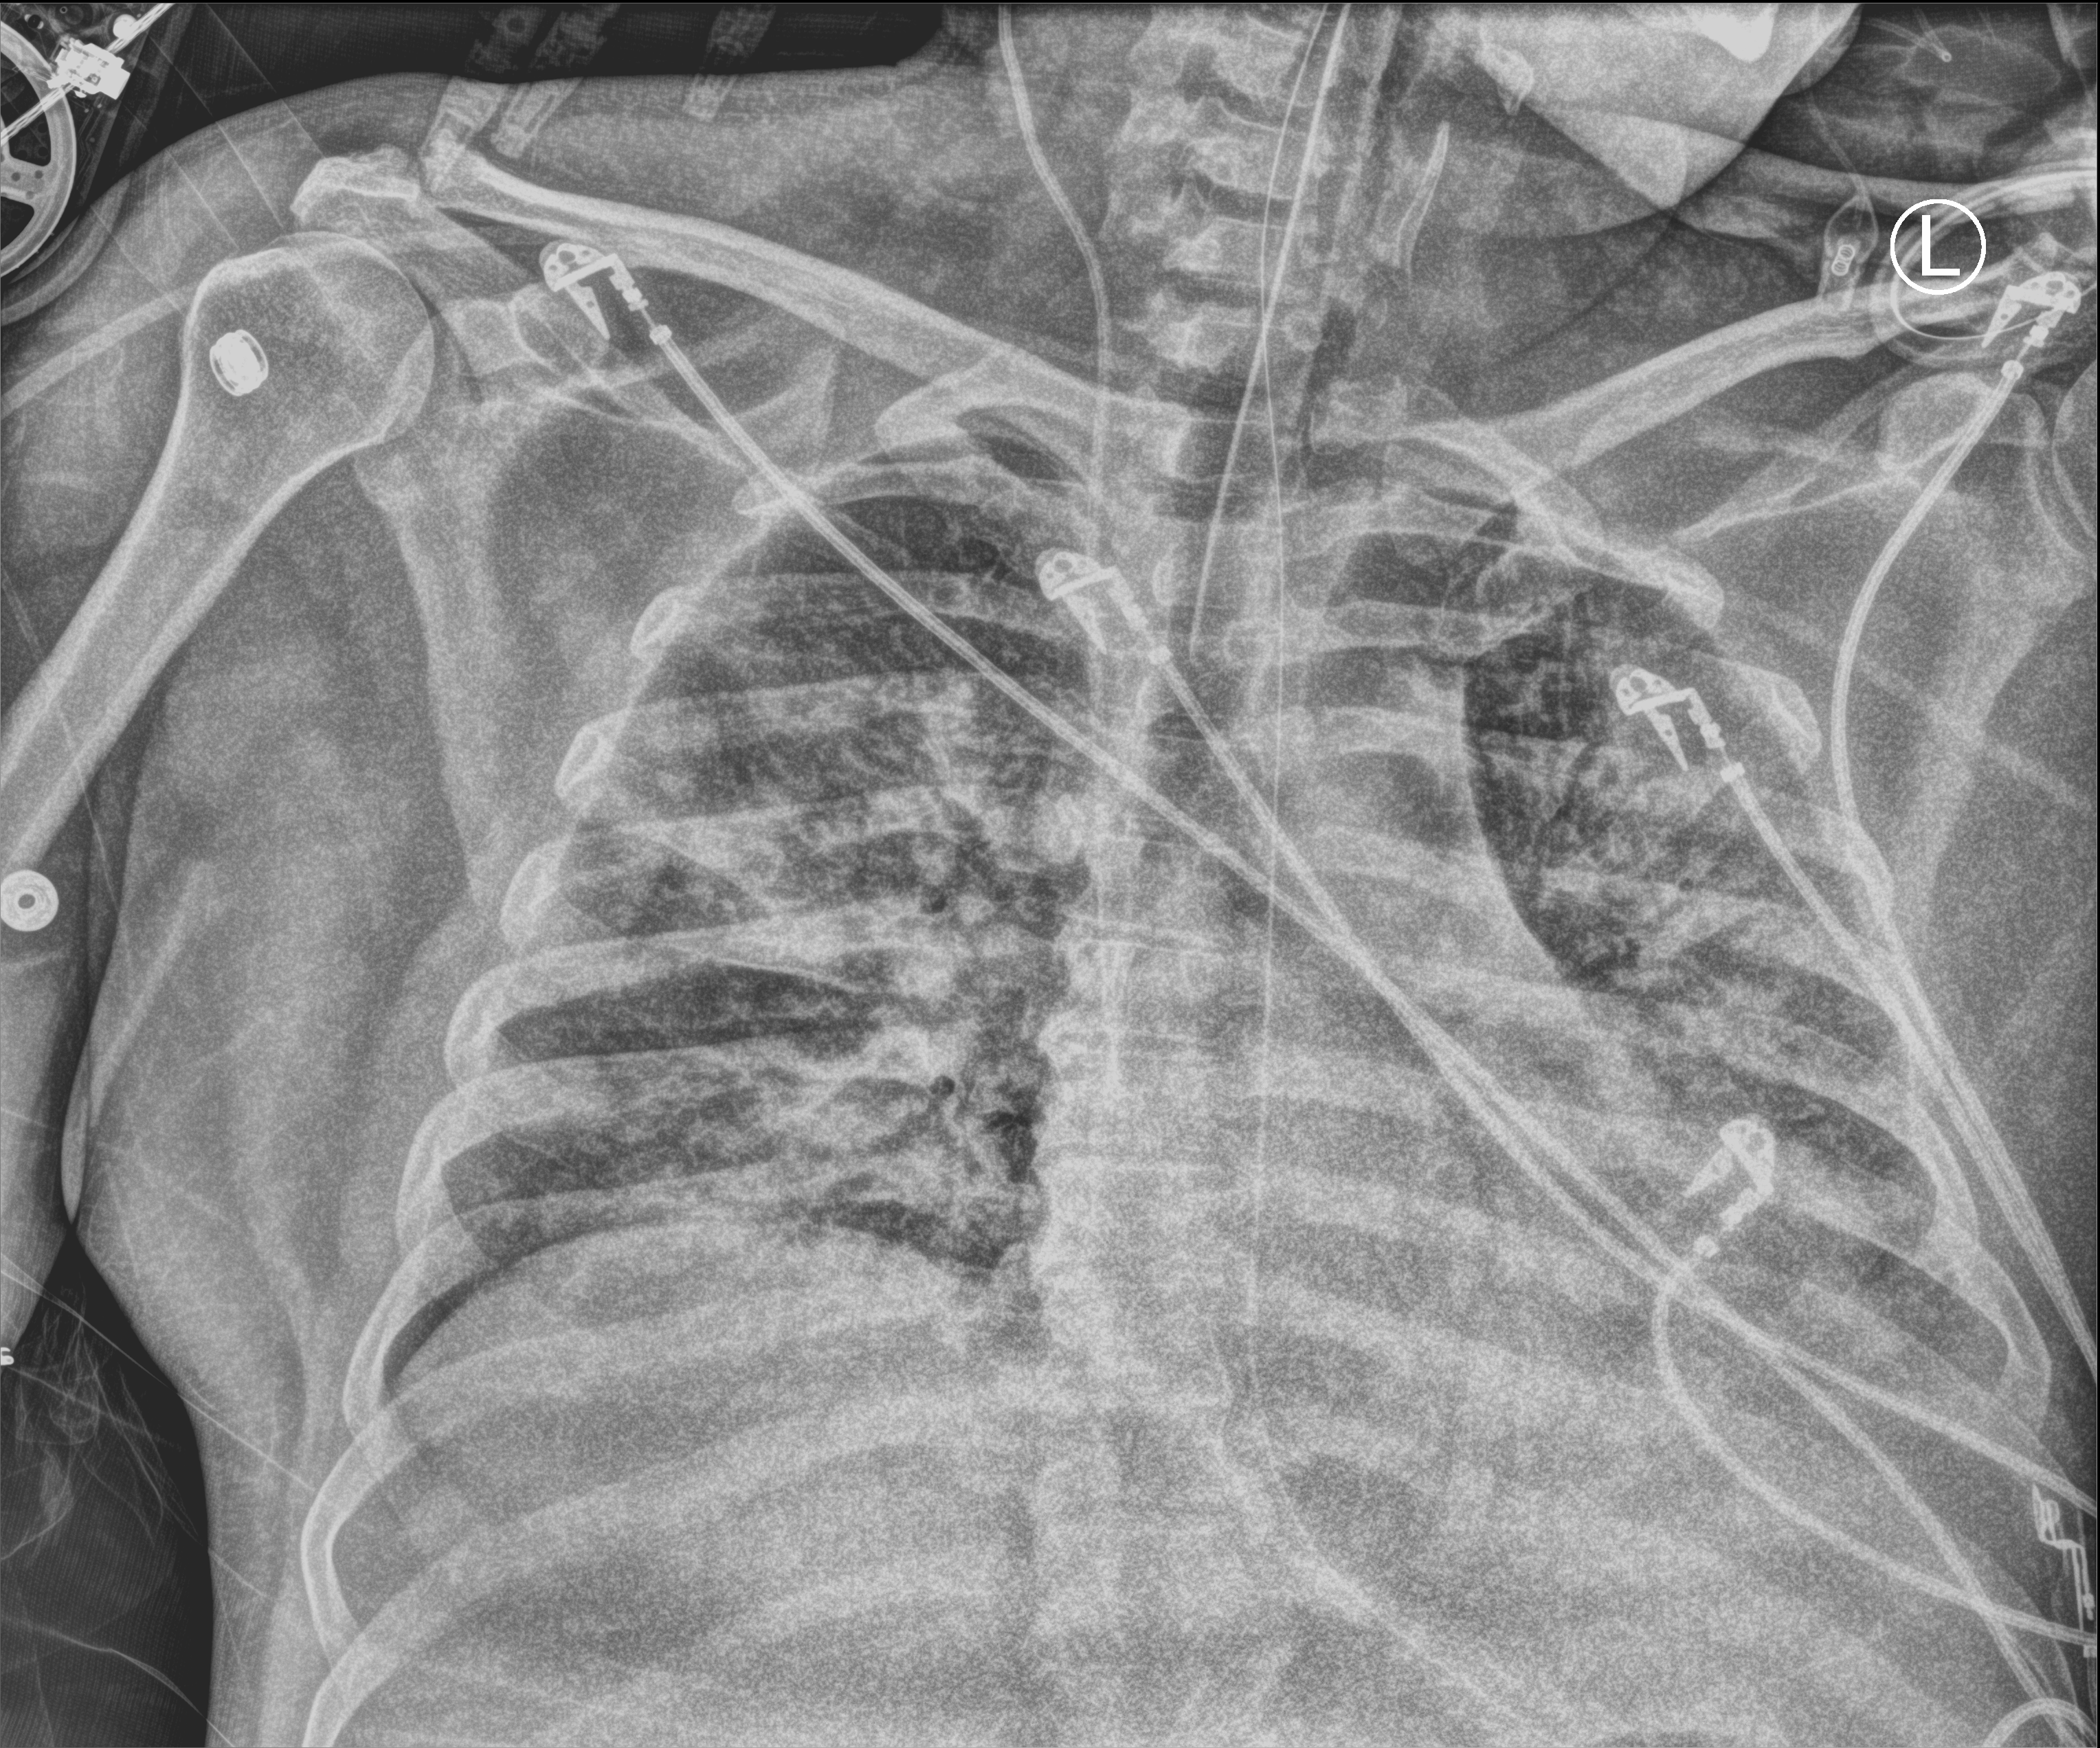
Chest X-ray (portable); anteroposterior (AP) projection. Patient hospitalised with COVID-19; male, aged 18–59 years.
From the hospital-stay record, not from the radiograph (when in the stay this image was taken is not recorded): smoking status (admission record): never; mechanically ventilated during this hospital stay: yes.